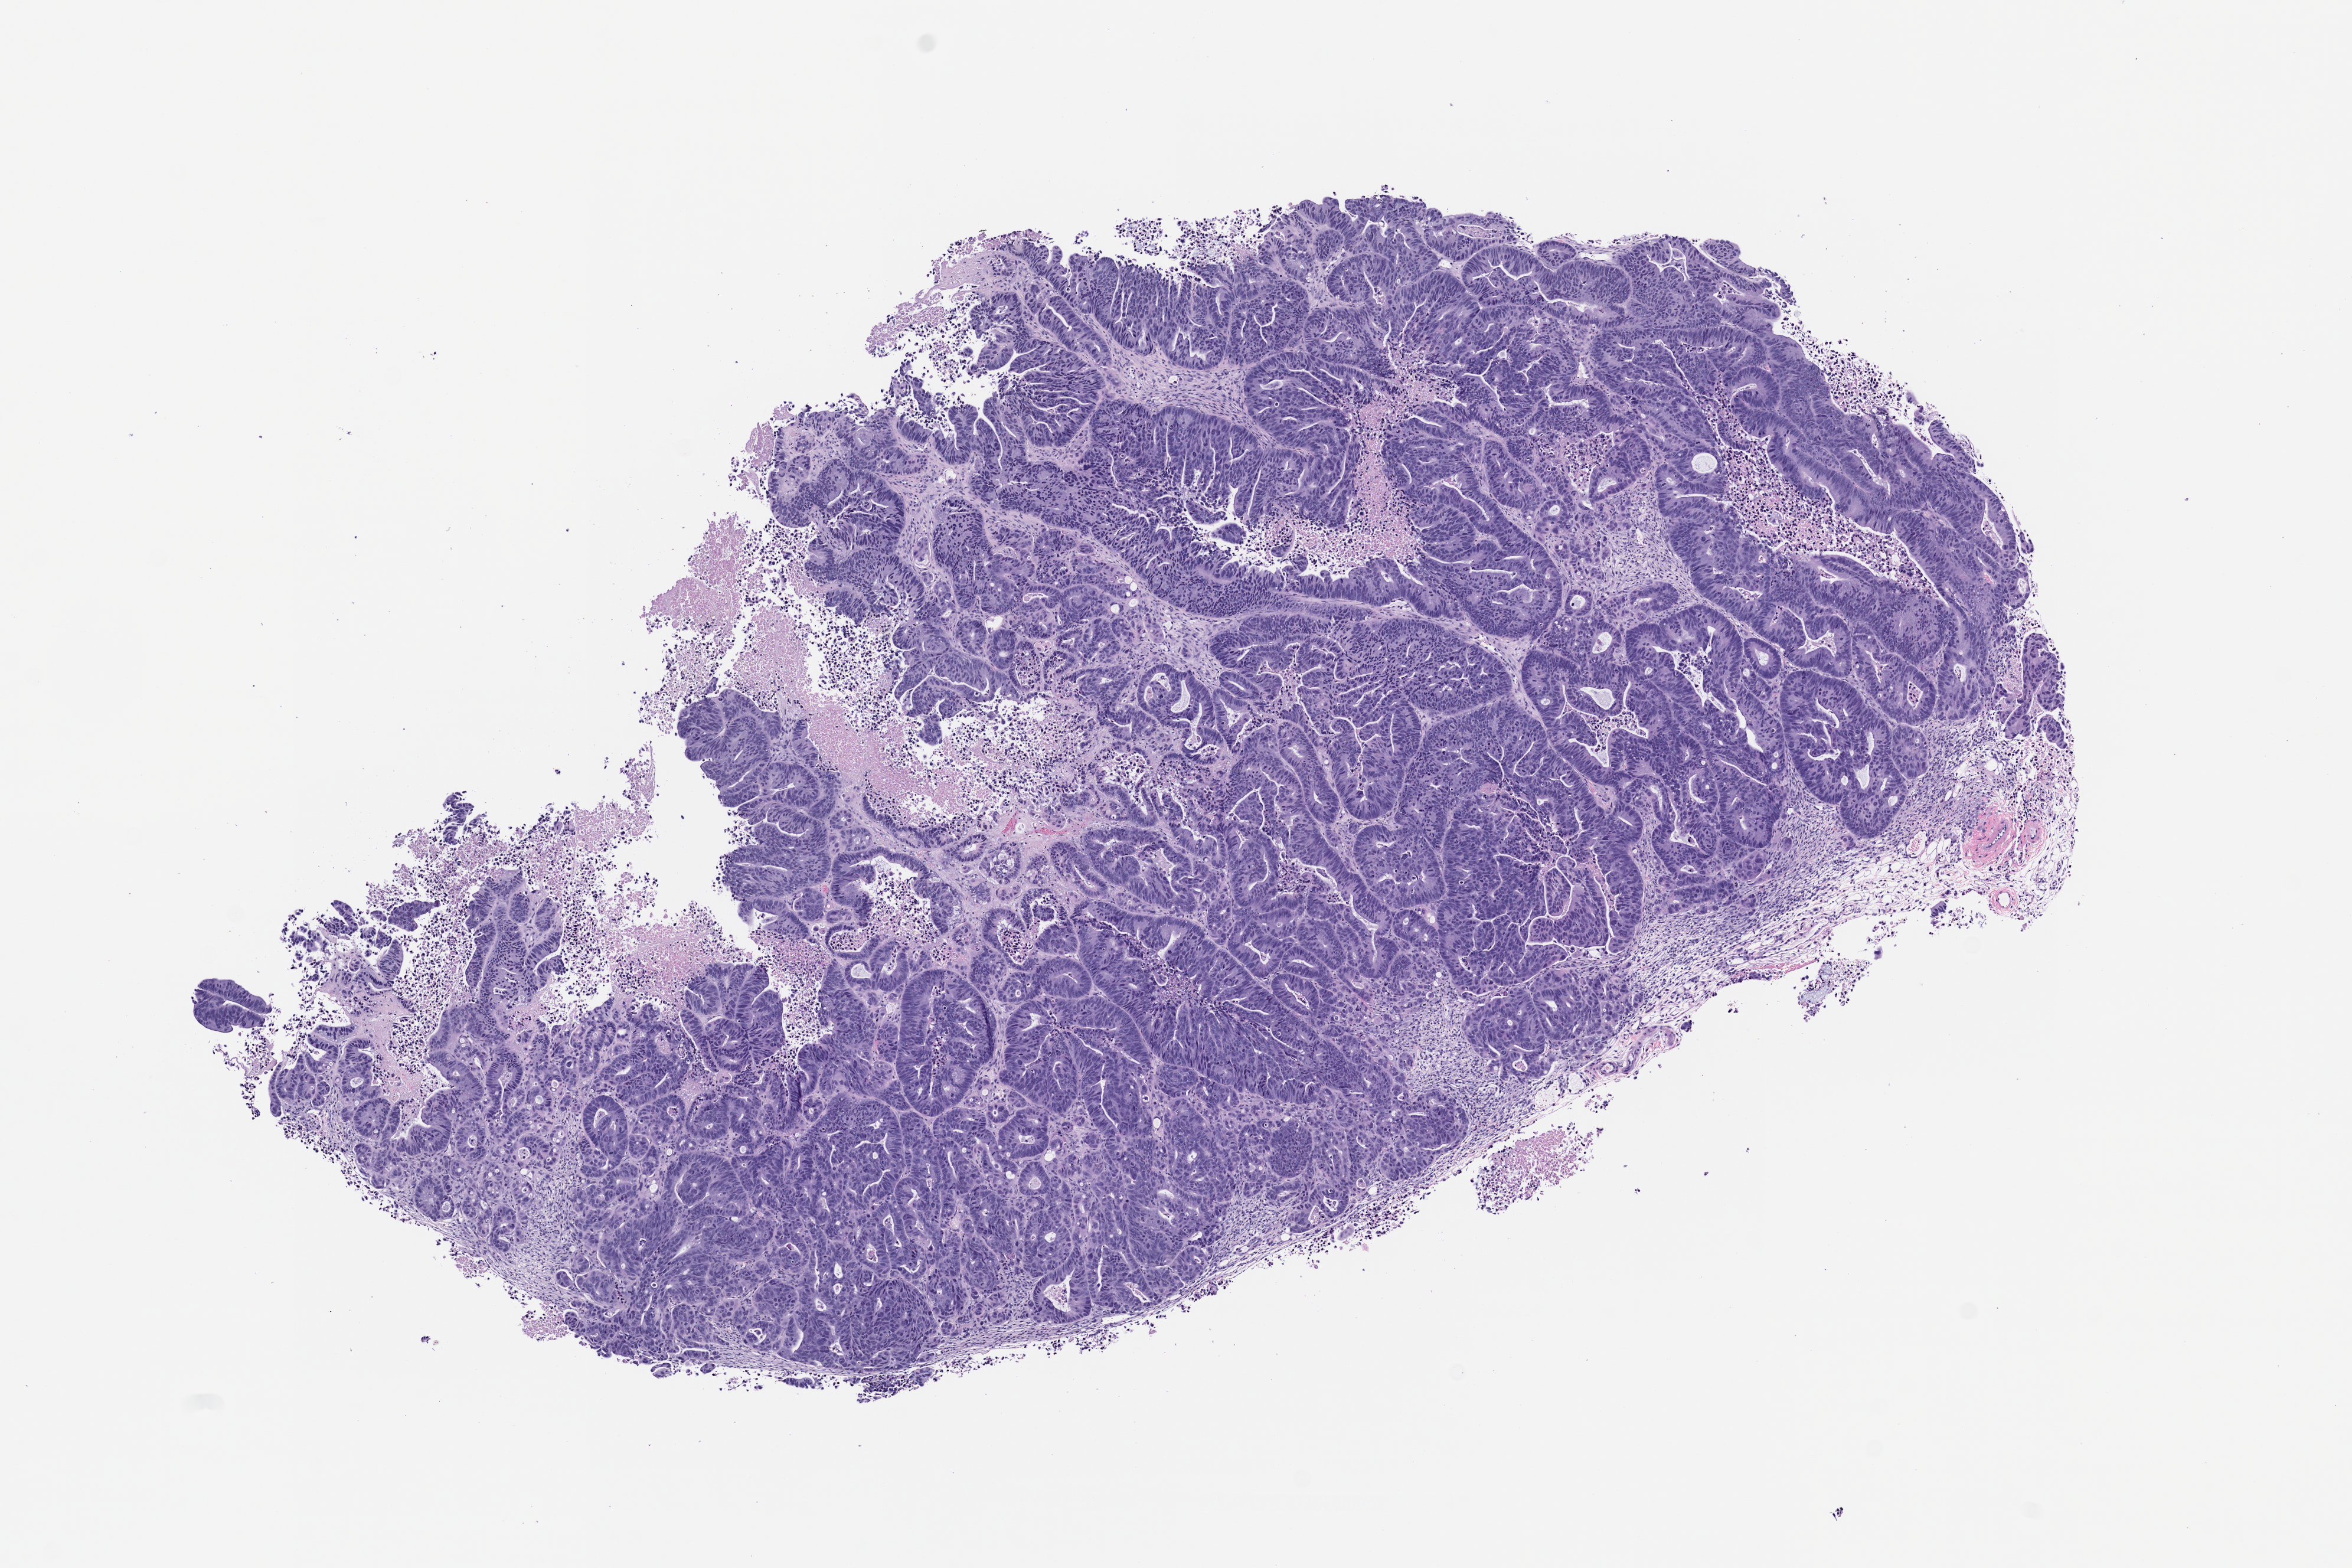
Whole-slide image, H&E: patient-derived xenograft (human tumor grown in a mouse), passage 2 — low-resolution overview of the scanned area, about 8.0 x 5.3 mm. Formalin-fixed, paraffin-embedded (FFPE) tissue. Tumor site category: rectum.
Originating patient diagnosis: Rectal Adenocarcinoma.